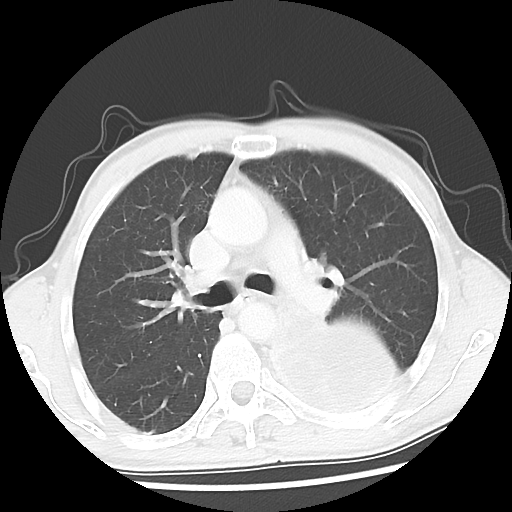
Chest CT, one axial slice. Slice 32 of 52 in the series (ordered by position). Reconstruction kernel LUNG. Lung window (W 1500 / L -600 HU). 5 mm slice thickness. 512 × 512 image matrix. Patient: male, 60 years. From the clinical record (not read from this slice): clinical TNM (as recorded): T4 N0 M0.
Outlined on this slice (bounding box drawn by a radiologist):
- lung tumour (recorded histology: squamous cell carcinoma): box from (x=261, y=302) to (x=408, y=427) px